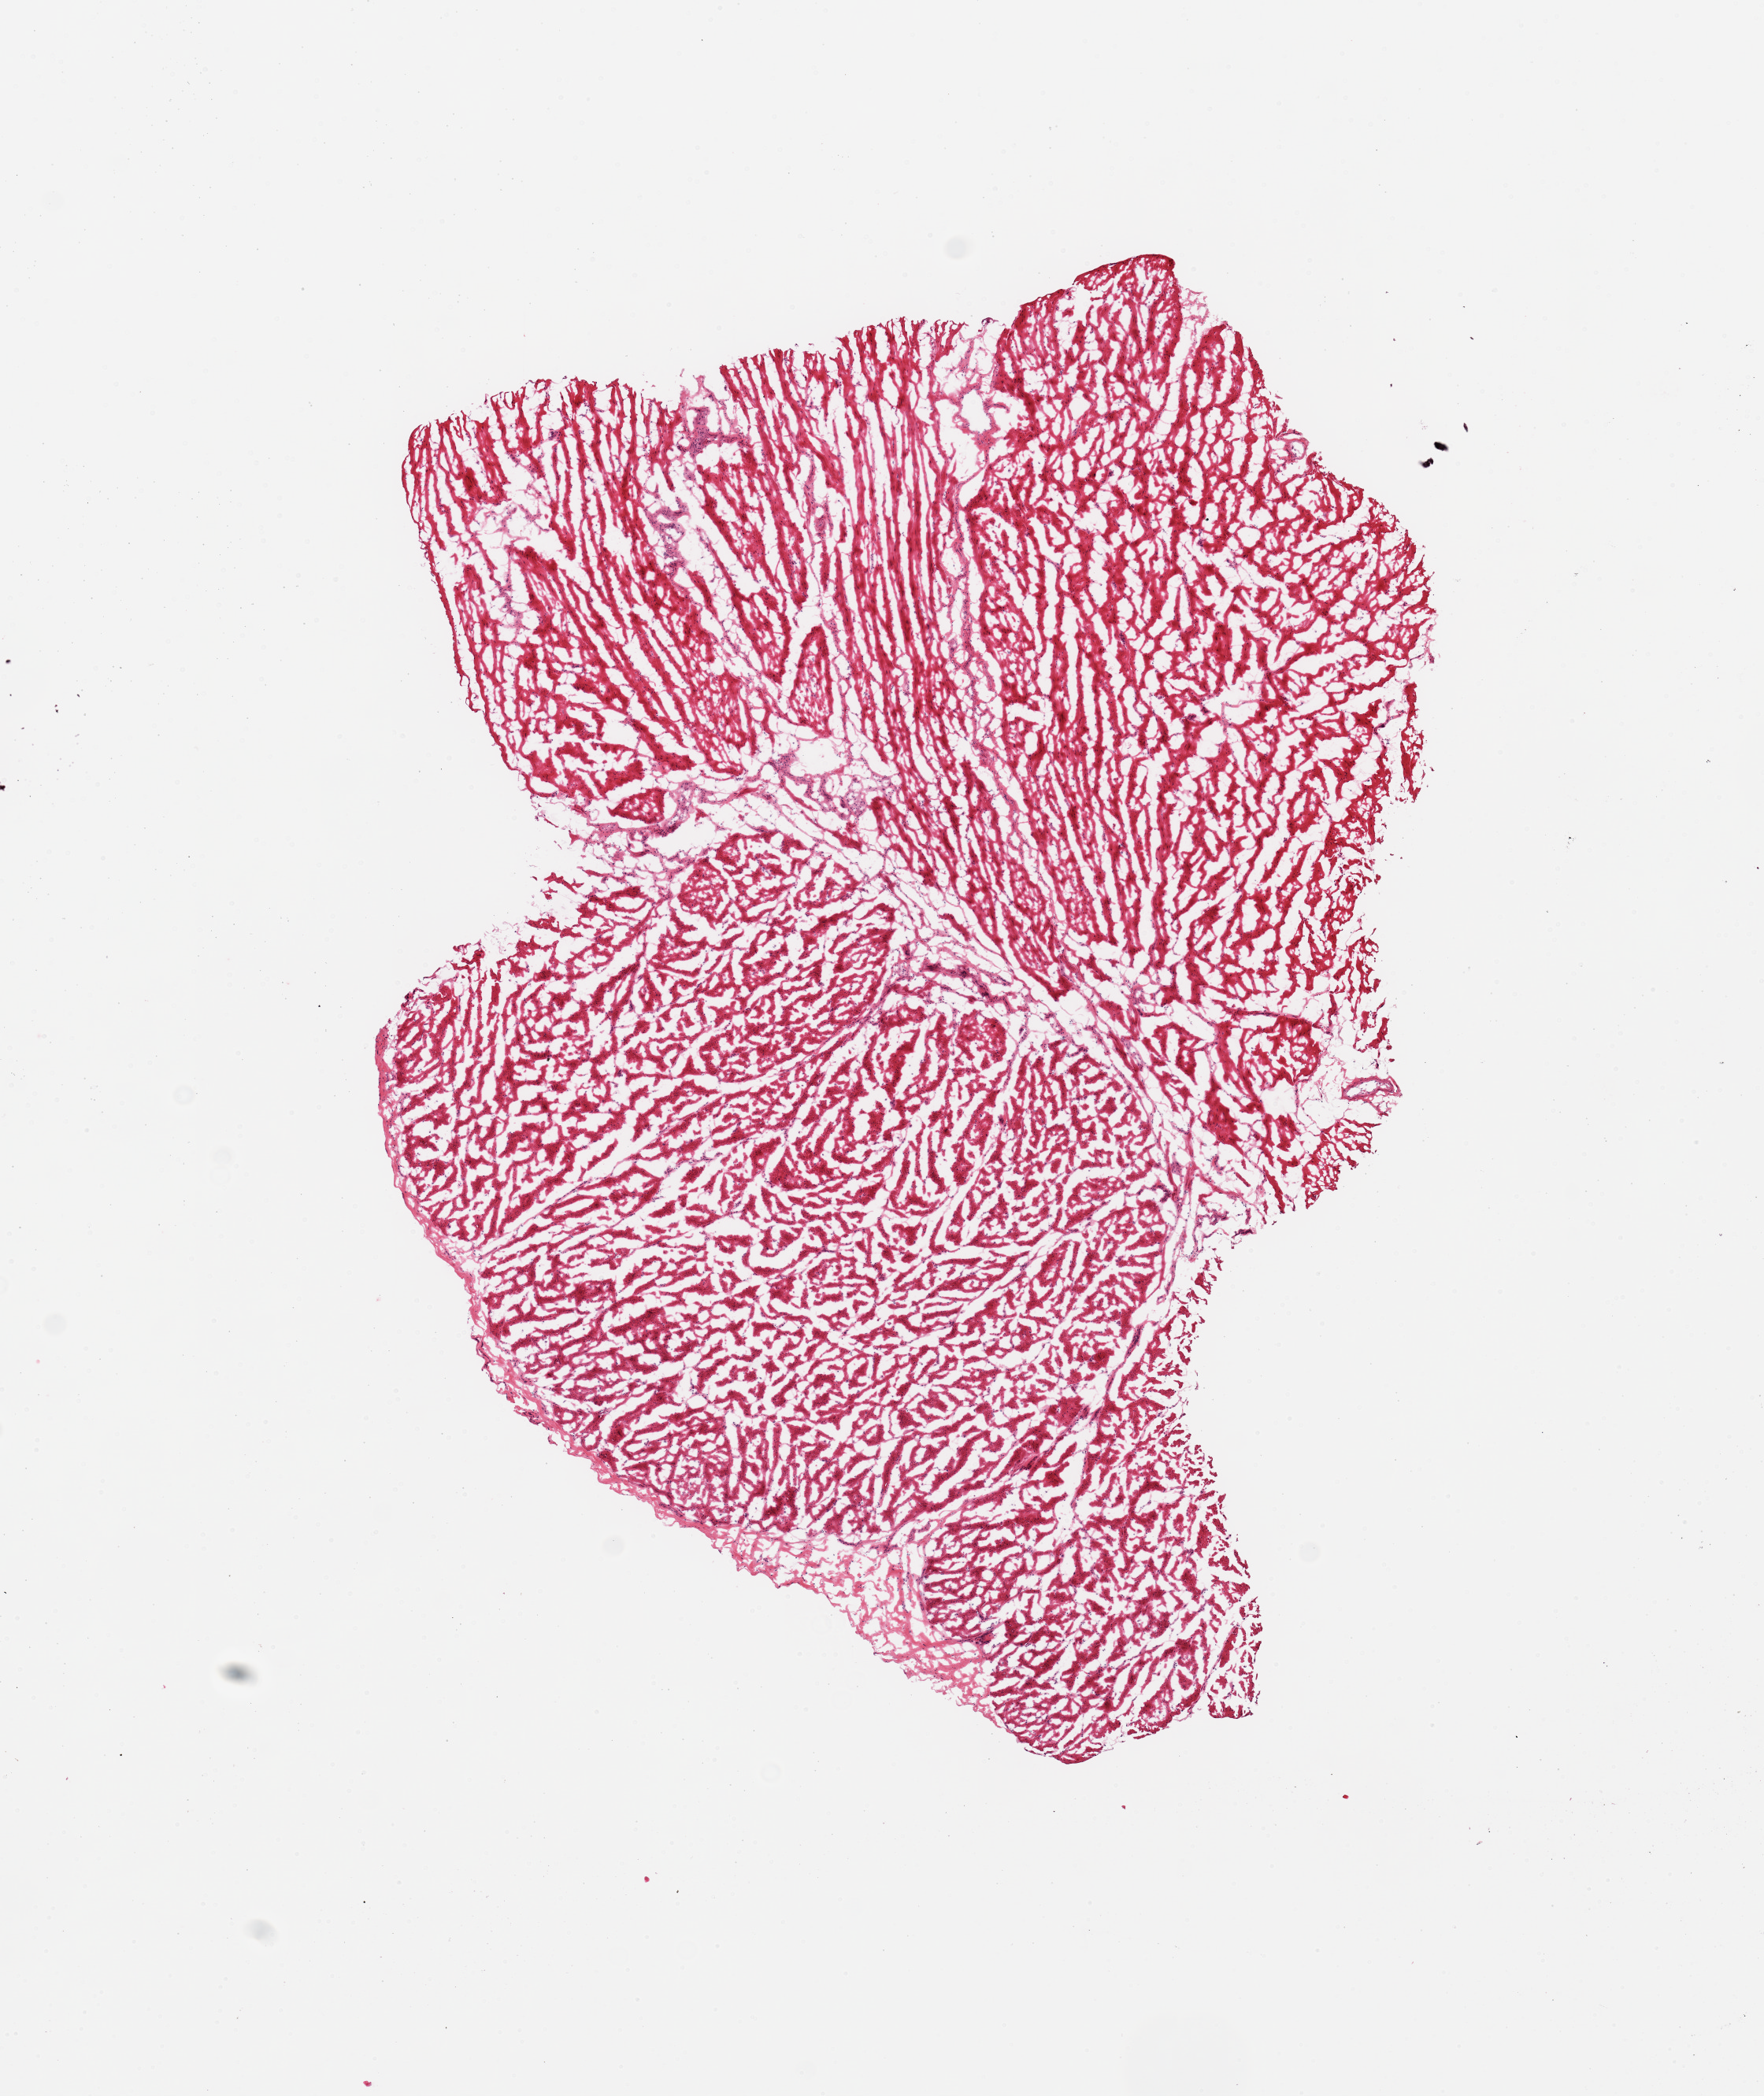
Digitized H&E-stained section, whole scanned area (about 8.9 x 10.5 mm, acquisition: 20x scan) shown as a low-resolution overview. Donor sex: male.
Specimen: frozen section; section of esophageal muscle (target tissue); tissue donor sample.